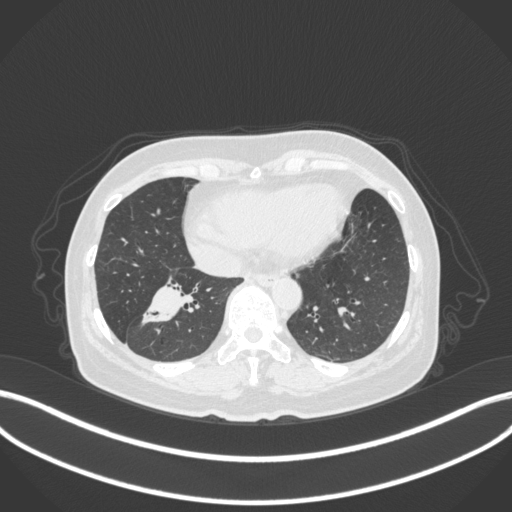
Chest CT, one axial slice; slice 123 of 429 in the series (ordered by position); reconstruction kernel B31f; lung window (W 1500 / L -600 HU); 1 mm slice thickness; 512 × 512 image matrix, field of view 400 × 400 mm. Patient: female, 67 years. Case-level facts recorded for this patient, not image findings: clinical TNM (as recorded): T1c N1 M0; histopathological grade: G2-3.
Structures marked on this image (bounding box drawn by a radiologist):
- lung tumour (recorded histology: adenocarcinoma): bounding box [x1, y1, x2, y2] px = [140, 275, 204, 331]